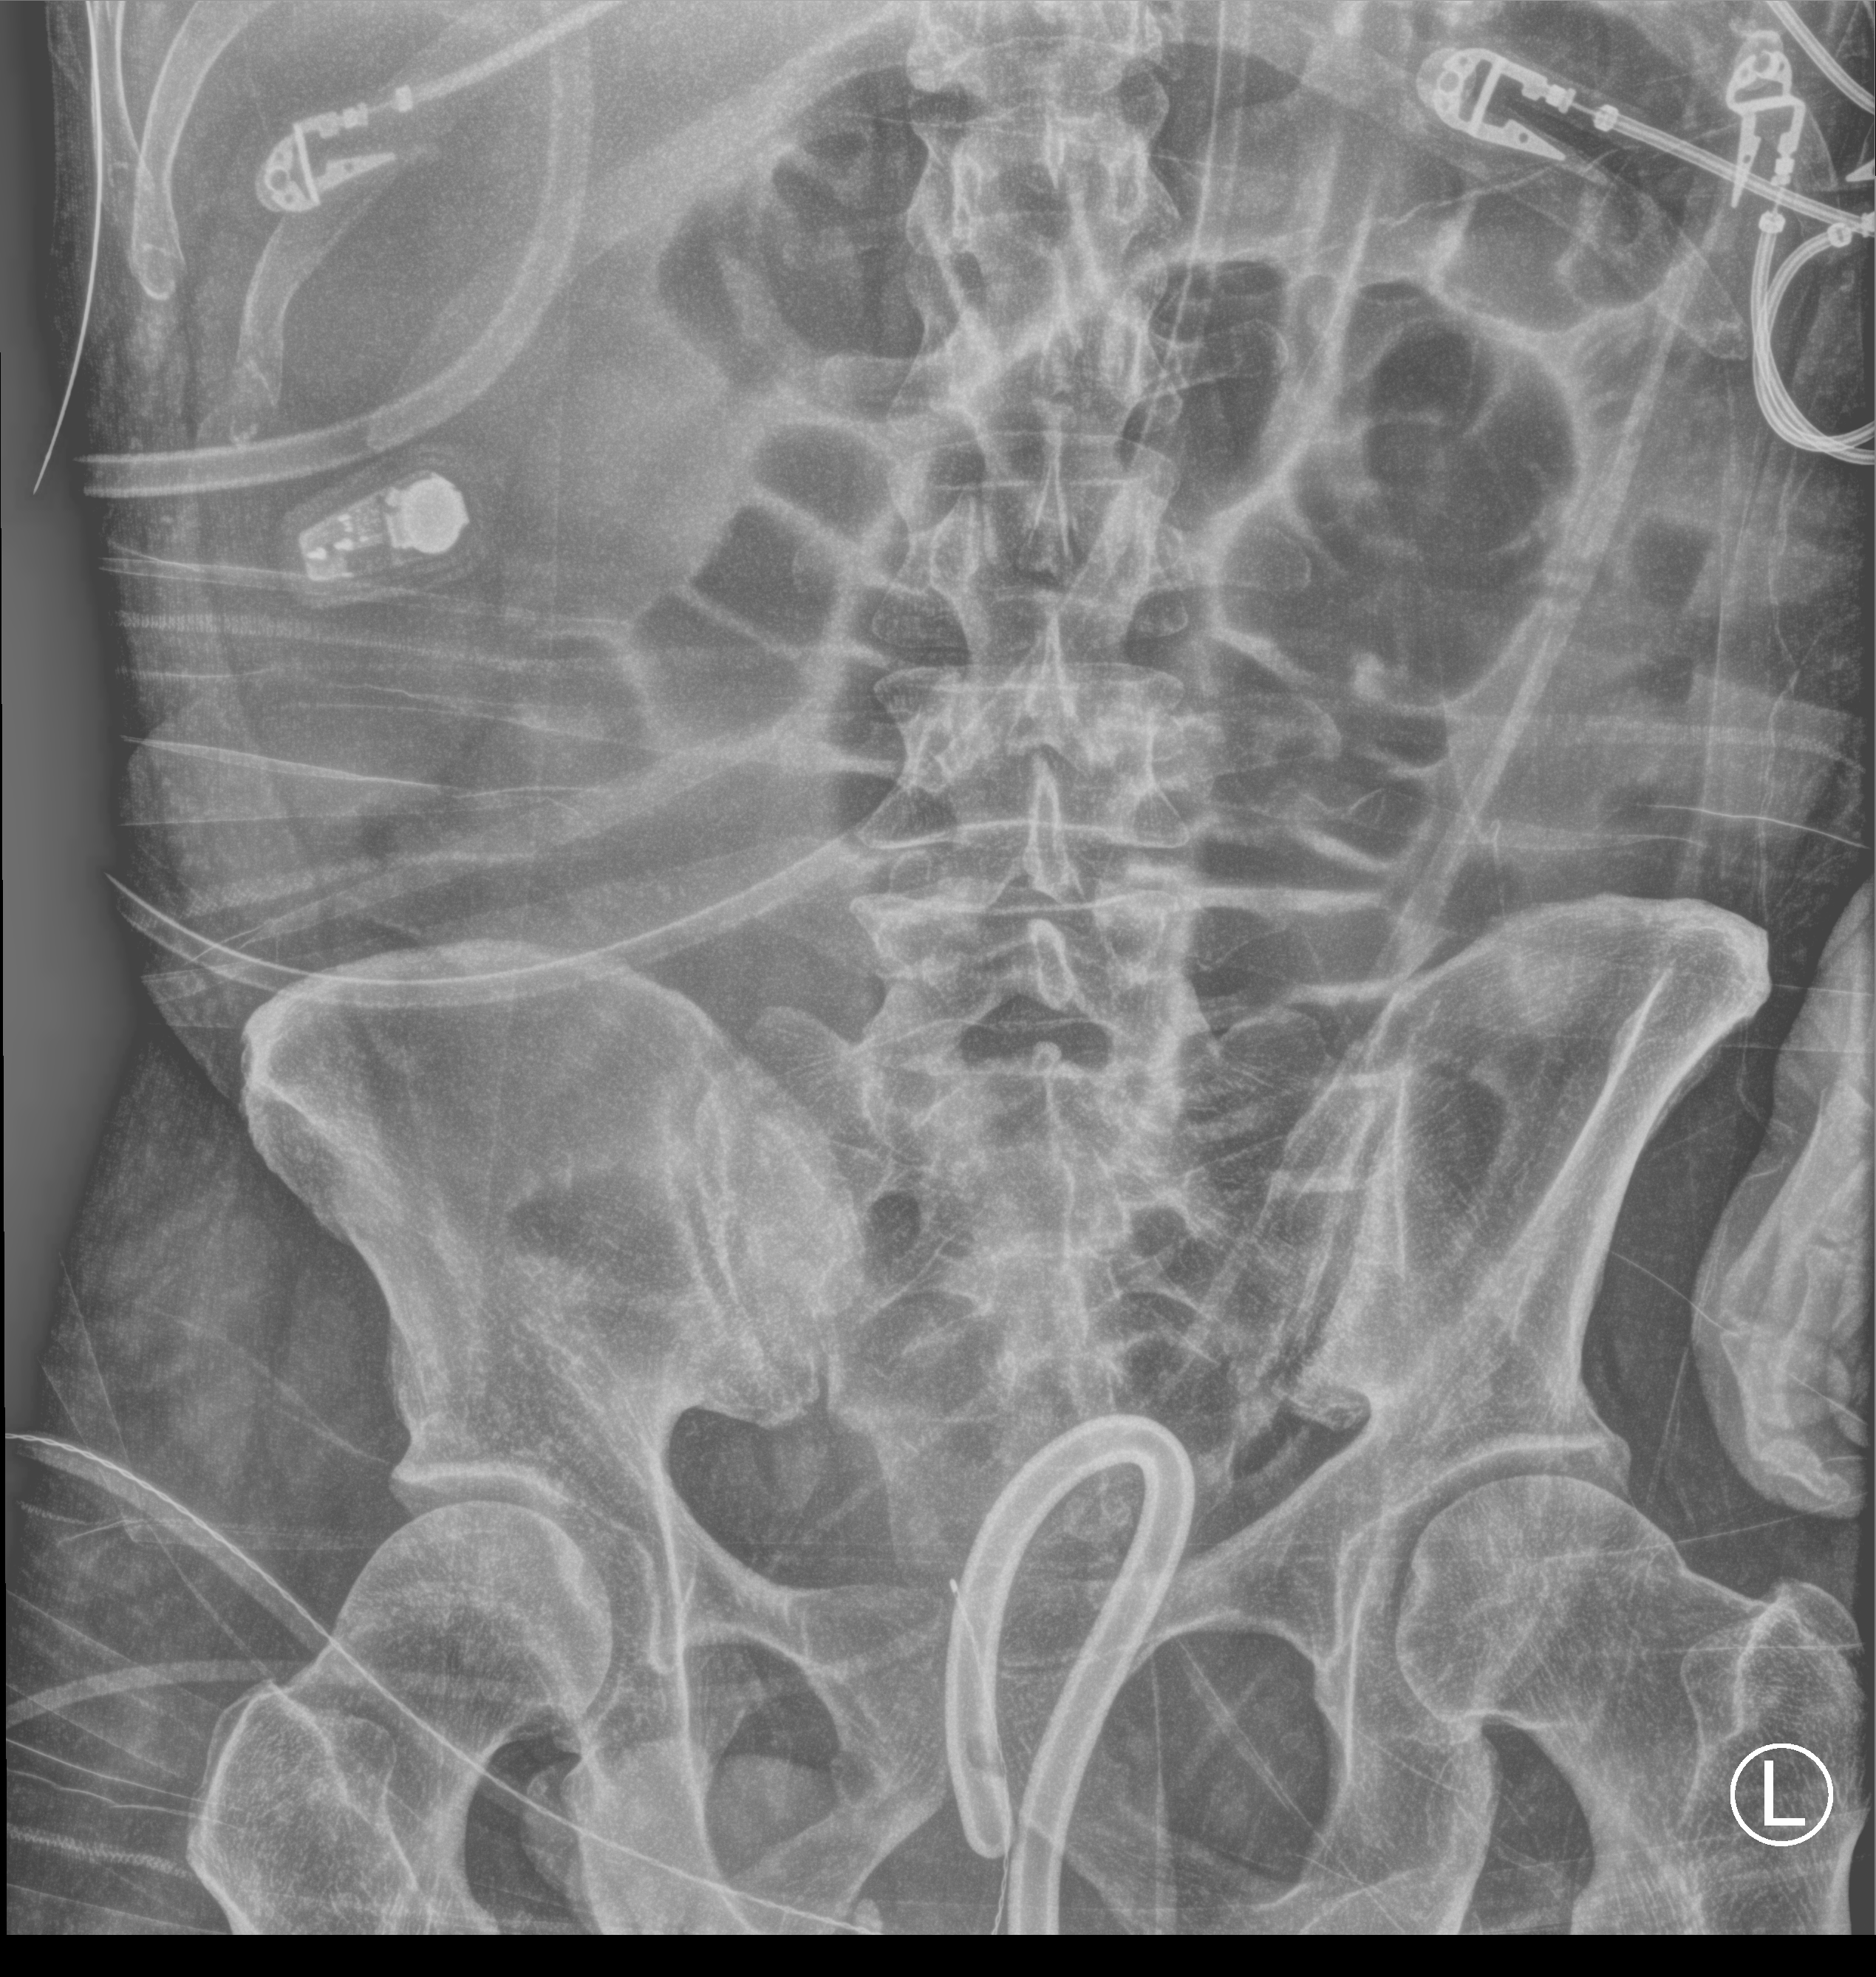
Bedside abdomen radiograph (computed radiography). Patient hospitalised with COVID-19; male, aged 18–59 years.
Admission-level facts for this patient (not findings on this image; timing relative to this image not recorded): admitted to intensive care during this hospital stay: yes; mechanically ventilated during this hospital stay: yes.